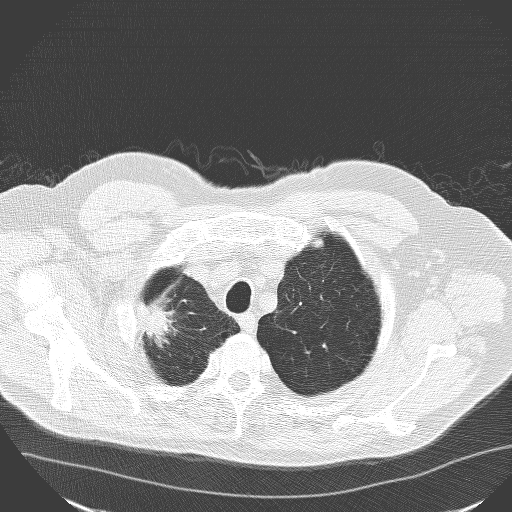
Low-dose screening chest CT, one axial slice; position 142 of 160 along the scan axis; 120 kVp; lung window (W 1500 / L -600 HU); 3.2 mm slice thickness; 512 × 512 image matrix, field of view 400 × 400 mm.
Annotated regions visible in this slice (expert manual segmentation):
- lesion 1 (tumor, upper lobe of right lung): box from (x=139, y=304) to (x=170, y=339) px